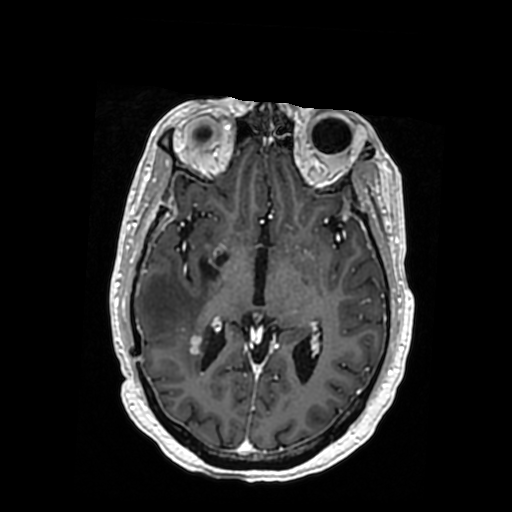
Brain MRI from a brain-tumour surgery series, one axial slice; slice 194 of 364 in the series (ordered by position); T1-weighted post-contrast; 0.5 mm slice thickness; 512 × 512 image matrix, field of view 260 × 260 mm. From the clinical record (not read from this slice): histopathology: Oligodendroglioma; WHO grade: 3; IDH mutation: yes.
Outlined on this slice (manually delineated by an expert):
- previous resection cavity: box from (x=201, y=253) to (x=228, y=277) px
- tumour: (x=170, y=333)–(x=181, y=350)